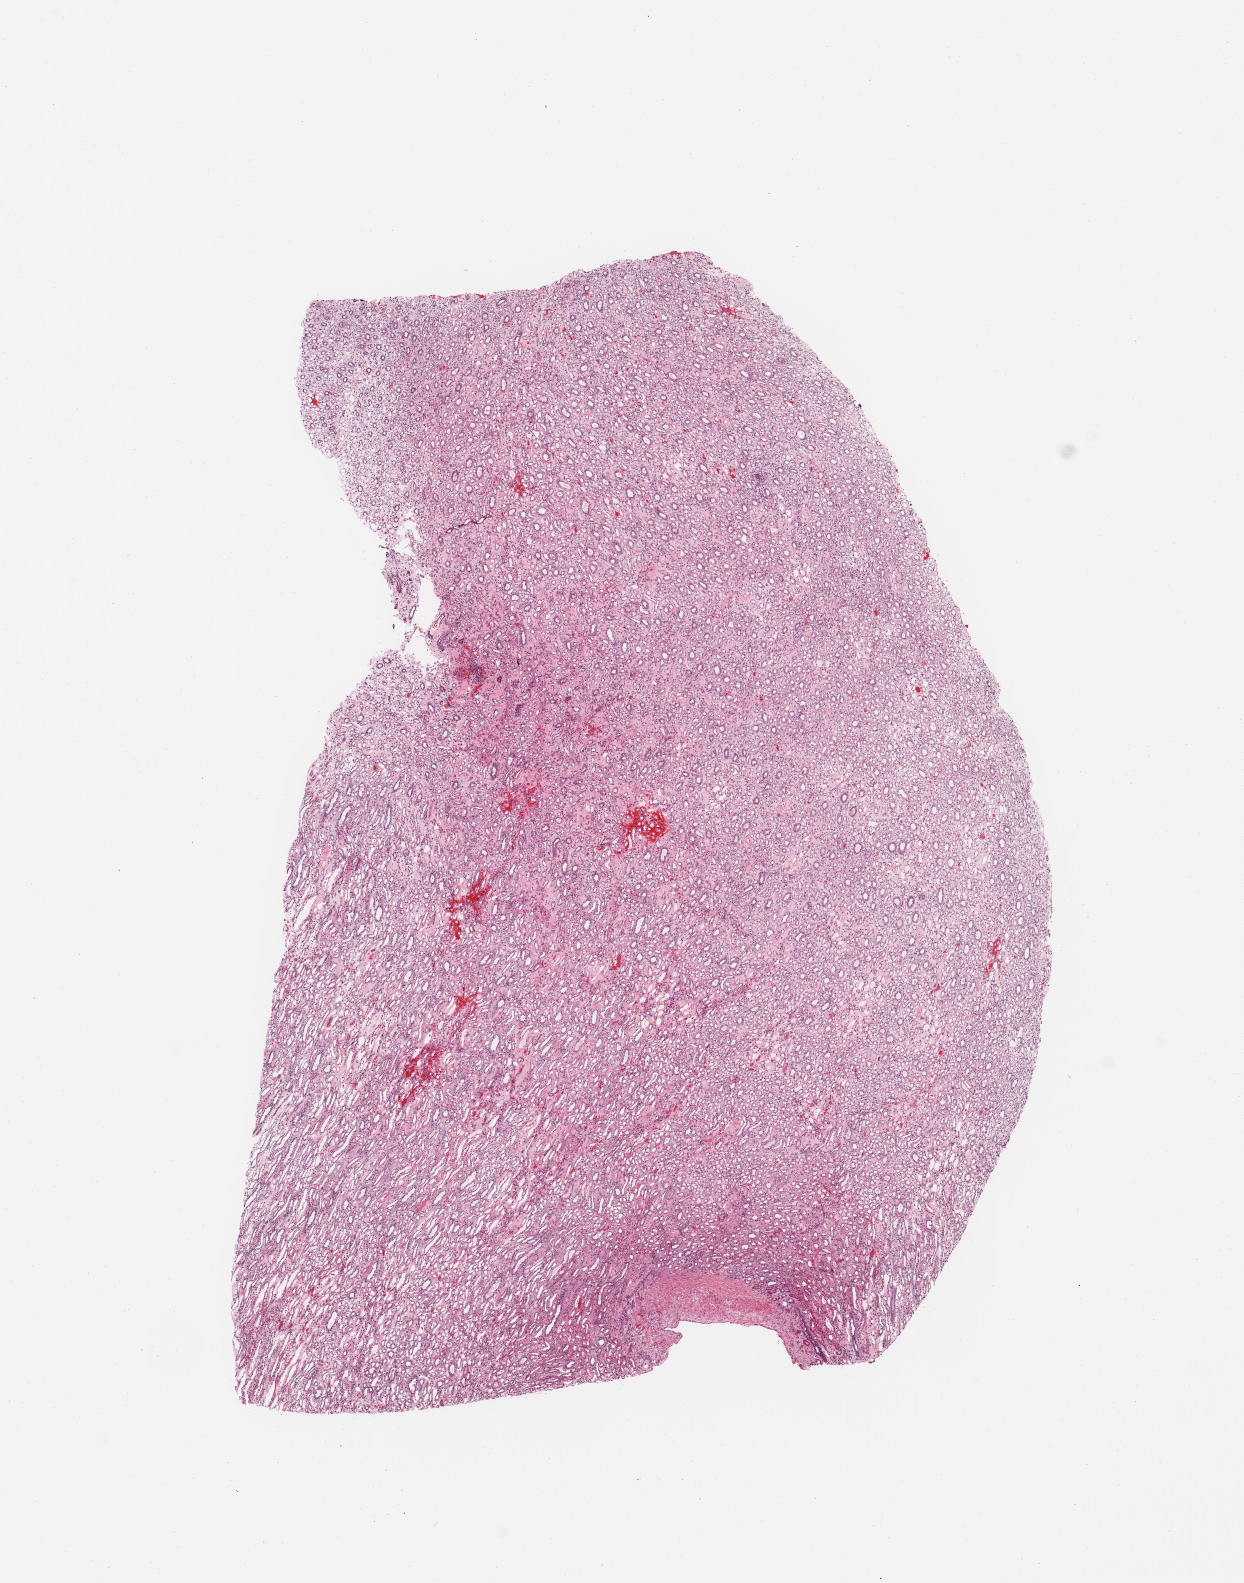
Digitized H&E tissue section (whole slide) — a low-resolution overview of the entire scanned area, about 9.8 x 12.5 mm (slide scanned at 20x), normal (non-tumour) tissue sample, sampled site: kidney. Male, 50 y/o.
This section: normal (non-tumour) tissue from the same patient. Patient diagnosis: Renal cell carcinoma, NOS.